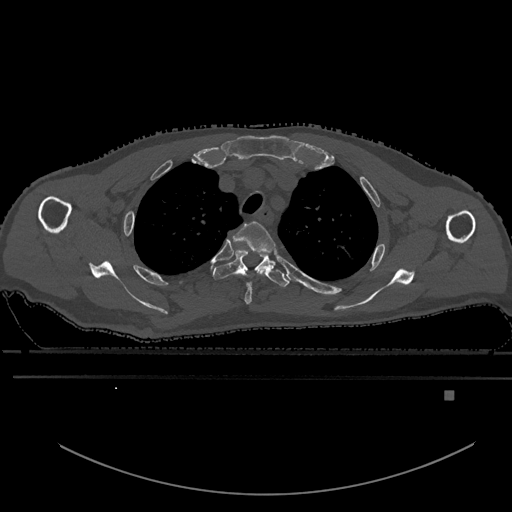
CT including the spine, one axial slice. Slice 468 of 969 in the series (ordered by position). Bone window (W 1800 / L 400 HU). 0.5 mm slice thickness. 512 × 512 image matrix. Patient: male, 82 years. Case-level facts recorded for this patient, not image findings: primary cancer: prostate; vertebrae with lytic lesions (as recorded): T11, T9, T8, T2.
Outlined on this slice (semi-automatic segmentation, software-assisted and operator-edited):
- T2 vertebra: box from (x=233, y=221) to (x=275, y=305) px
- T3 vertebra: (x=213, y=250)–(x=289, y=287)